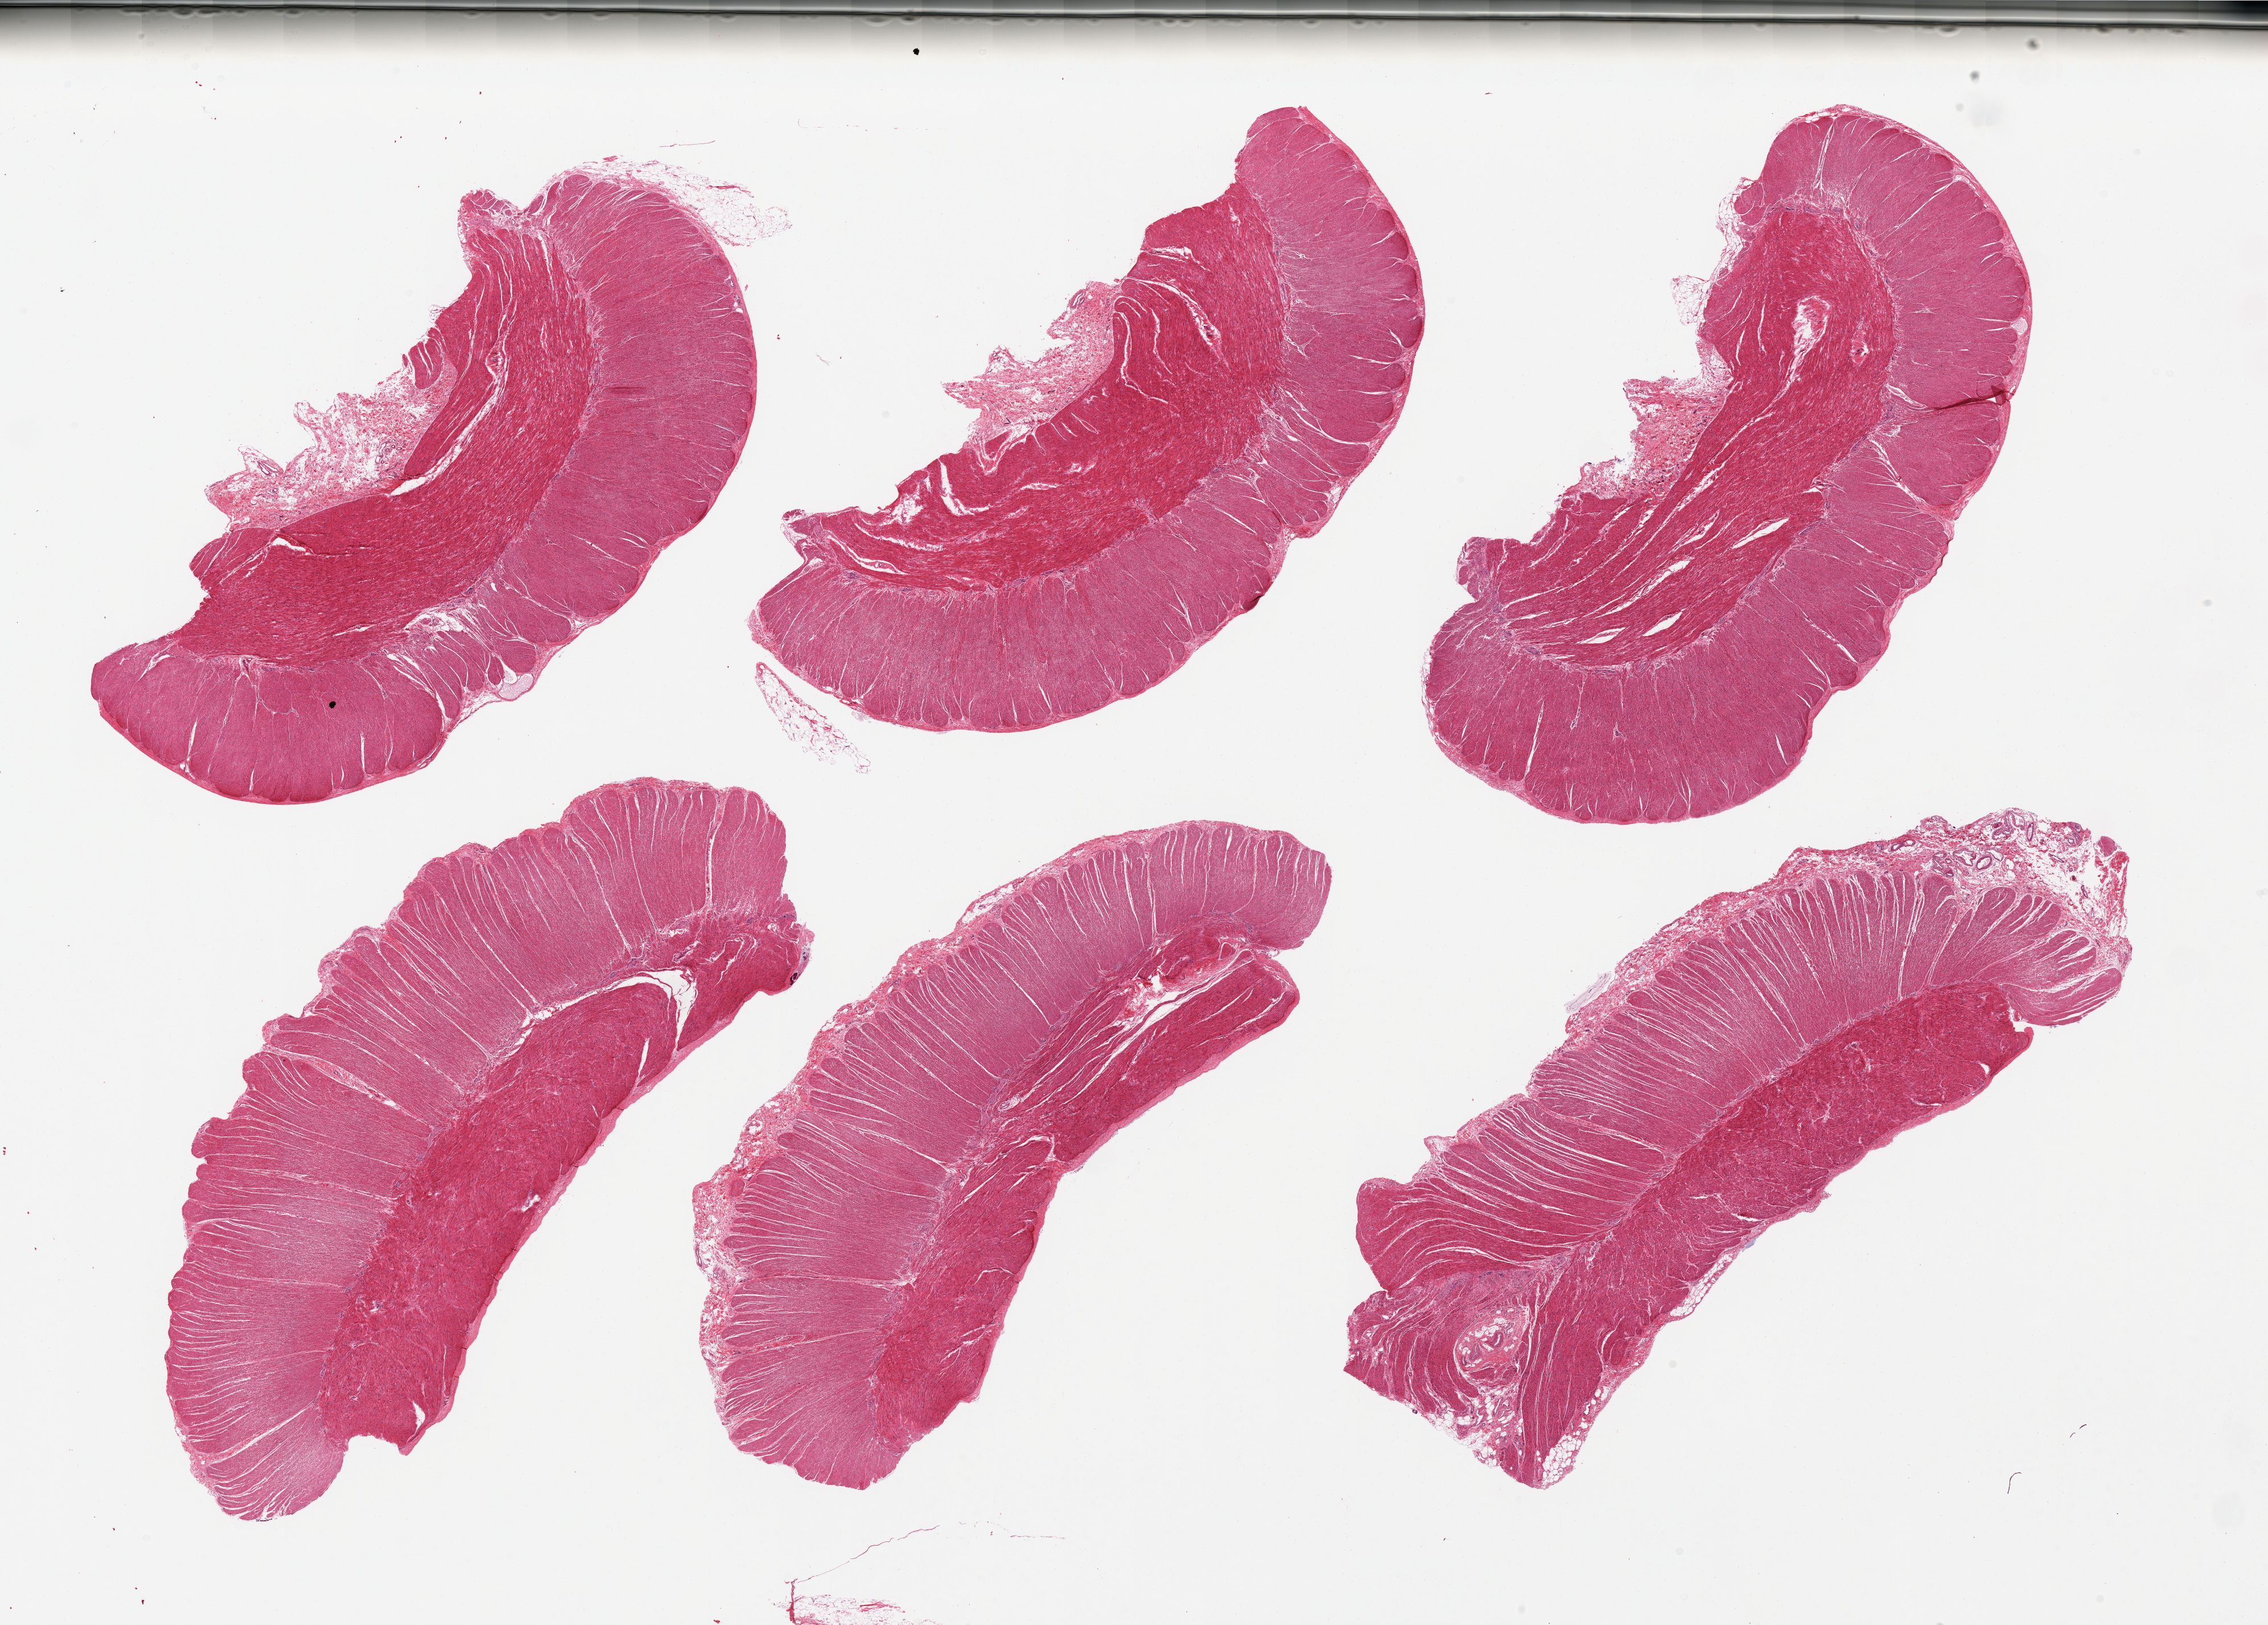
H&E whole-slide image, brightfield, a low-resolution overview of the entire scanned area, about 31.5 x 22.6 mm (acquisition: 20x scan), PAXgene-fixed paraffin-embedded (PFPE) section, section of sigmoid colon (target tissue), donor tissue sample. Donor sex: female.
* review note (as recorded): 6 pieces, all muscularis, good specimens